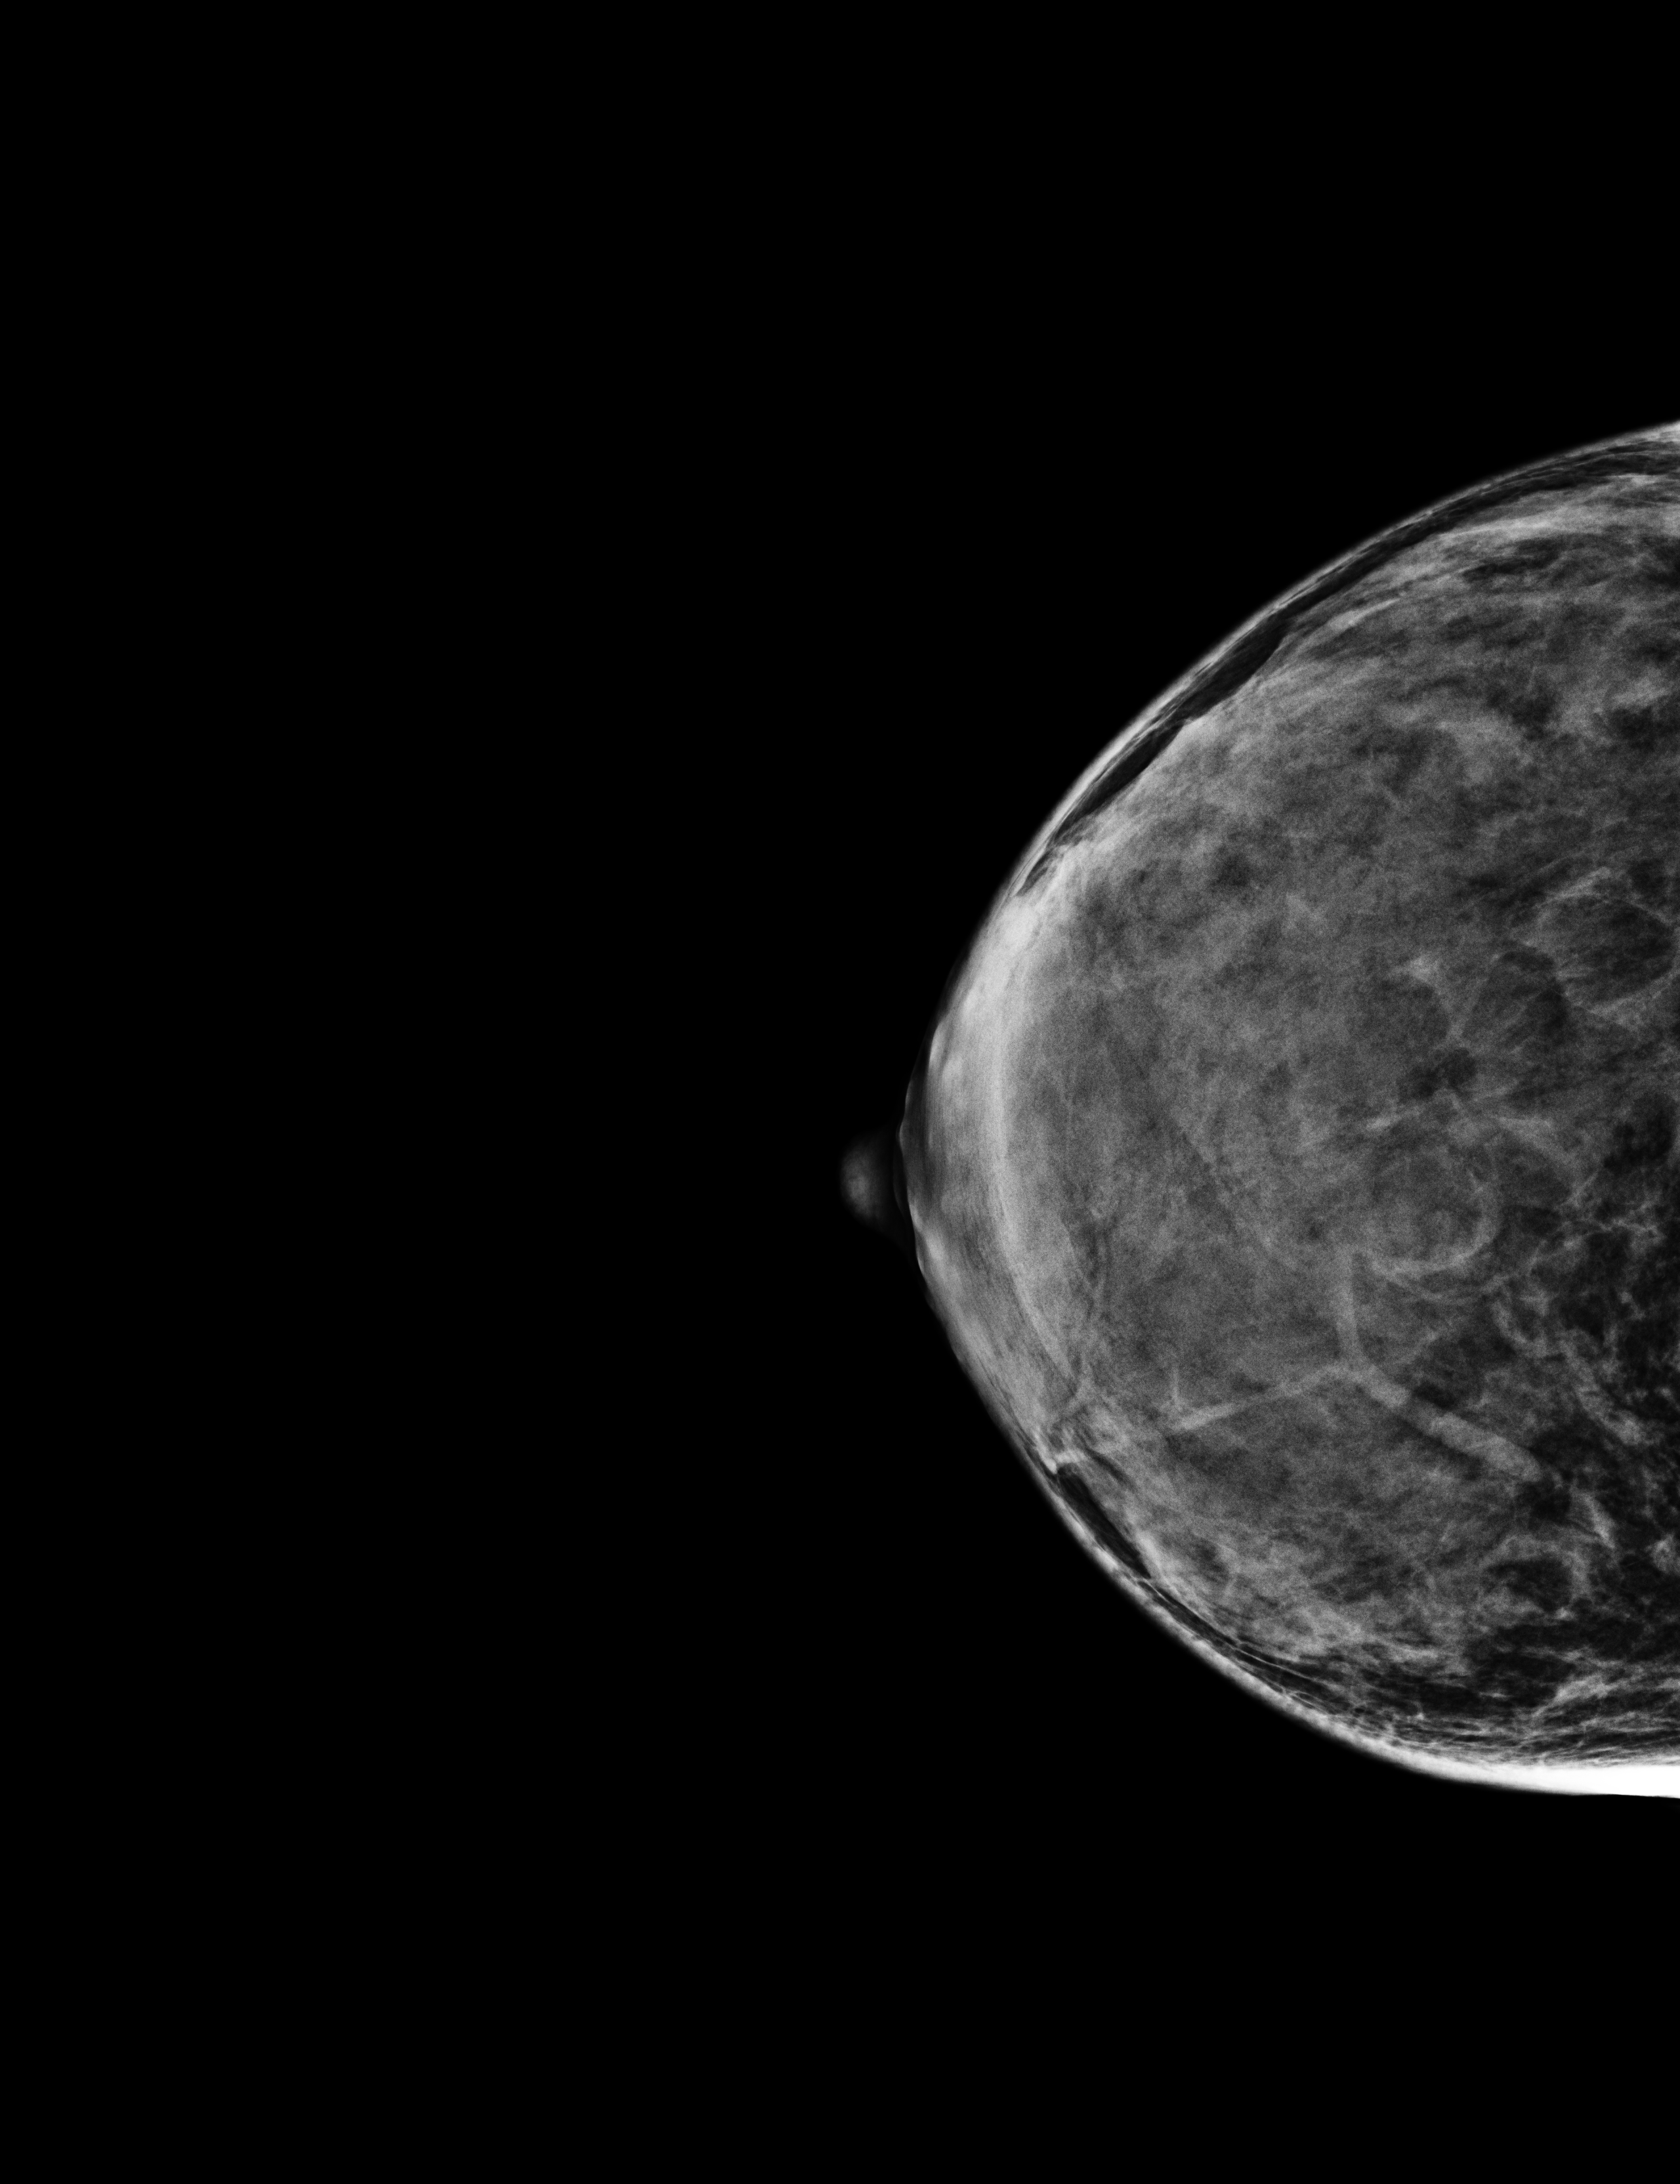
Screening examination, system: Selenia Dimensions.
Image type: full-field digital mammogram. Breast: right. Projection: cranio-caudal projection.